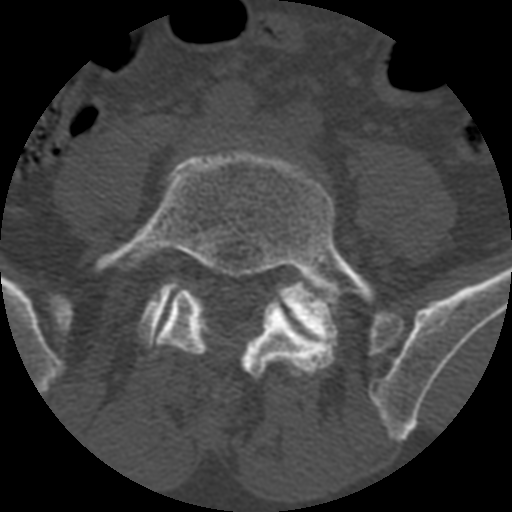
CT including the spine, one axial slice; position 255 of 399 along the scan axis; reconstruction kernel STANDARD; 120 kVp; bone window (W 1800 / L 400 HU); 512 × 512 image matrix, field of view 160 × 160 mm. Patient age 71 years. Case-level facts recorded for this patient, not image findings: primary cancer: prostate.
Annotated regions visible in this slice (semi-automatic segmentation, software-assisted and operator-edited):
- L5 vertebra: box from (x=91, y=149) to (x=378, y=378) px